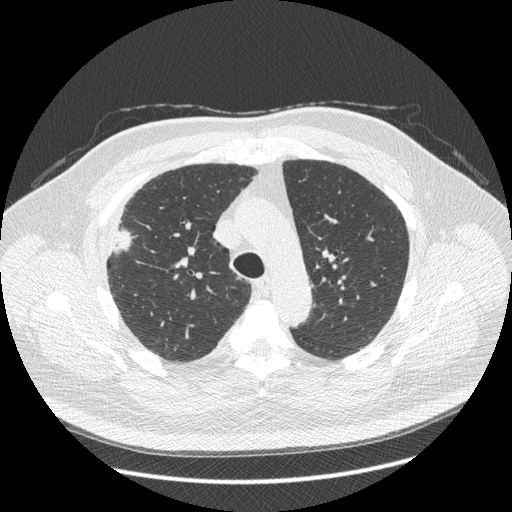
Low-dose screening chest CT, axial slice; third annual screen; lung window (W 1500 / L -600 HU); 120 kVp; slice 116 of 426 in the series. Male, age 66 years at enrolment.
Expert-annotated lung lesion, bounding box <88,208,148,270> (left, top, right, bottom; pixels). Reader record for this screening exam (exam-level; its link to the box is not recorded): non-calcified nodule or mass ≥4 mm, right upper lobe, 48 × 25 mm, spiculated (stellate) margins, soft tissue attenuation, pre-existing on the prior screen: no. Later outcome: lung cancer diagnosed 35 days after this screen — non-small cell carcinoma, right upper lobe, stage IV (AJCC 6th edition), 50 mm at pathology.